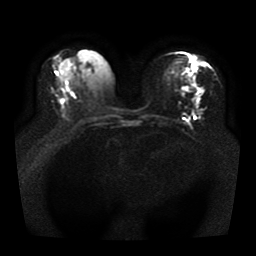
Breast MRI, one axial slice; position 17 of 41 along the scan axis; diffusion-weighted series; image 2 of 4 stored at this slice position (different b-values; order by instance number); 1.5 T; 5 mm slice thickness; 256 × 256 image matrix. Female patient.
Outlined on this slice (expert manual segmentation):
- tumour on diffusion-weighted imaging: bounding box [x1, y1, x2, y2] px = [197, 99, 200, 104]